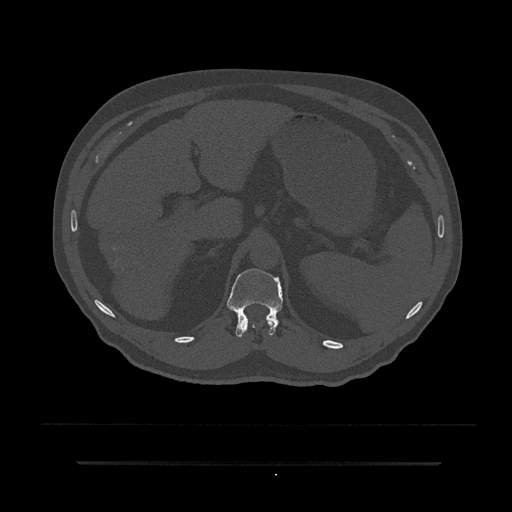
CT including the spine, one axial slice; position 231 of 797 along the scan axis; reconstruction kernel Br40s/3; 120 kVp; bone window (W 1800 / L 400 HU); 0.5 mm slice thickness; 512 × 512 image matrix. Male patient, age 59 years. From the clinical record (not read from this slice): primary cancer: bile ducts.
Structures marked on this image (semi-automatically segmented with operator editing):
- T11 vertebra: bounding box <244,319,275,330> (left, top, right, bottom; pixels)
- T12 vertebra: <227,268,283,337>